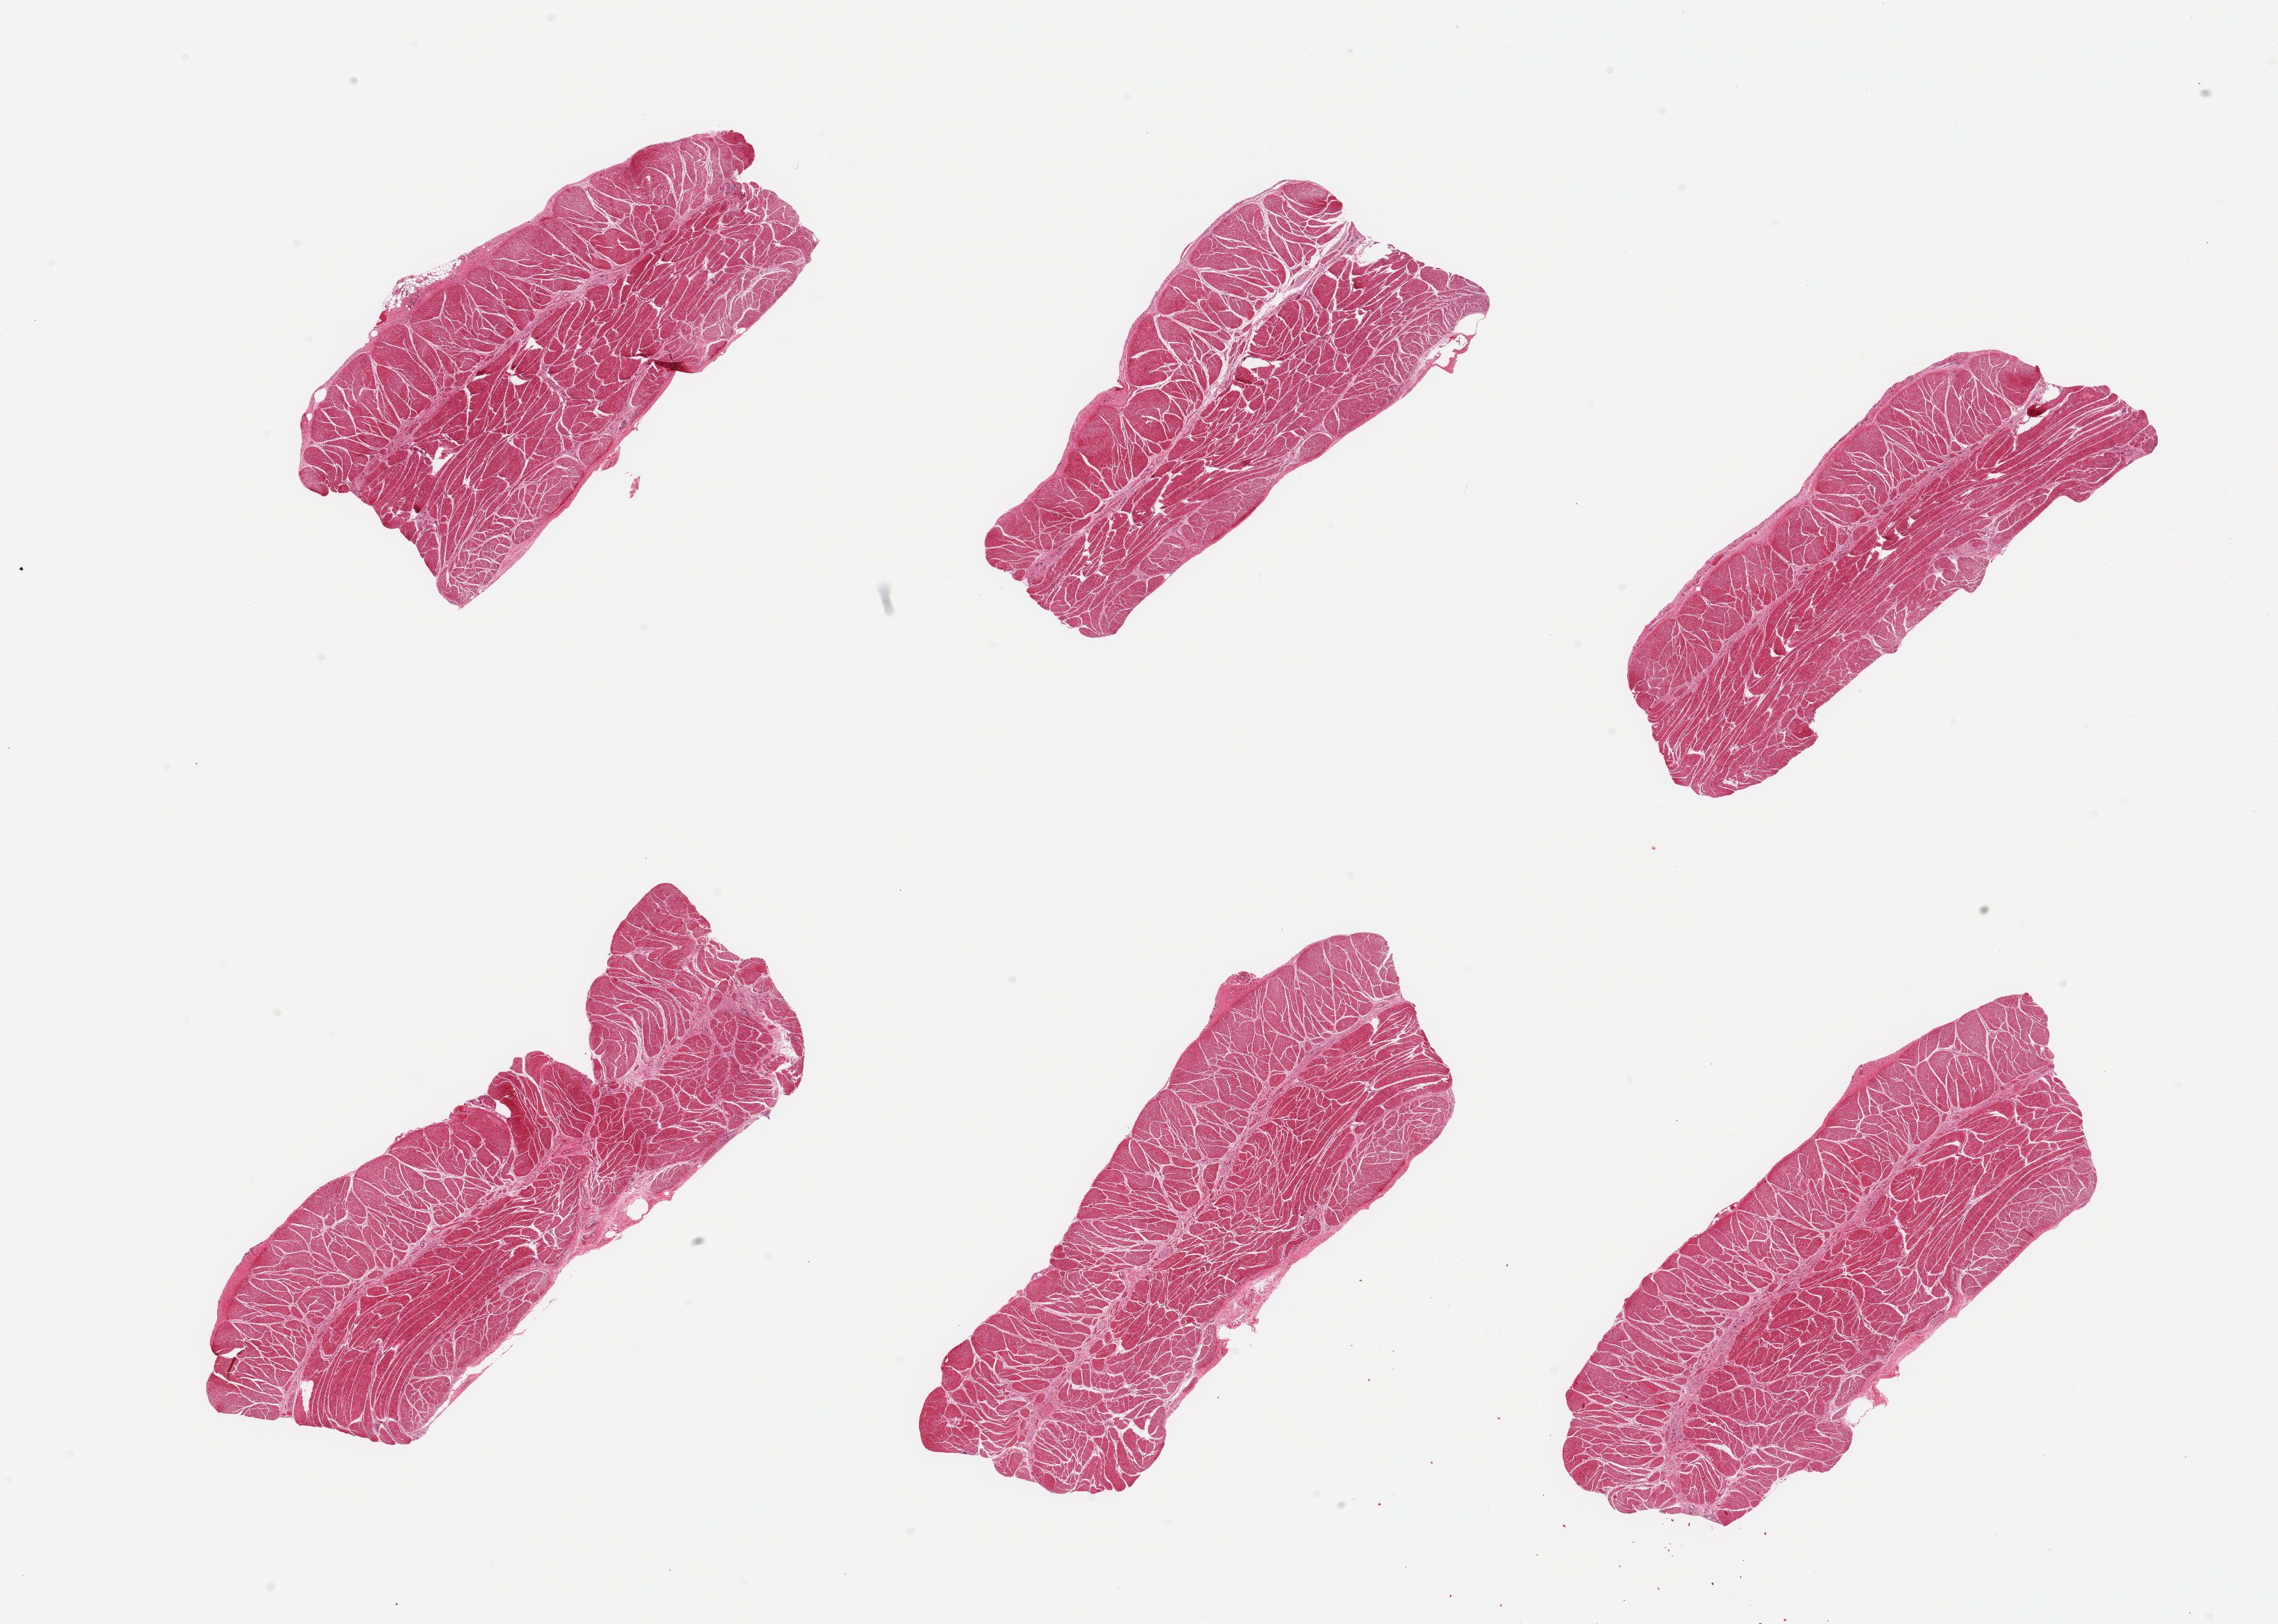
Whole-slide image, haematoxylin and eosin stain, a low-resolution overview of the entire scanned area, about 27.6 x 19.7 mm (slide scanned at 20x). PAXgene-fixed, paraffin-embedded tissue. Section of esophageal muscle (target tissue). Donor tissue sample. Donor: male.
Pathologist's review note for this sample: 6 pieces, confirmed target muscularis.